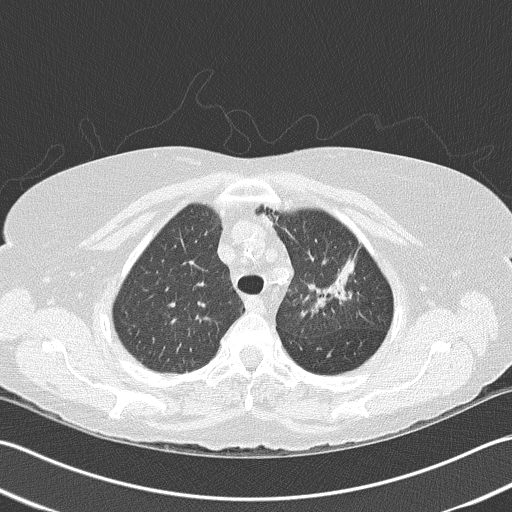
Chest CT (low-dose screening protocol), one axial image. Baseline screening round. Lung window (W 1500 / L -600 HU). 2 mm slice thickness. 512 × 512 image matrix. Female, age 68 years at enrolment. Former smoker at enrolment.
• Expert reader's lesion annotation, bounding box [x1, y1, x2, y2] px = [294, 239, 368, 318].
• Screening reader's record for this exam: no non-calcified nodule ≥4 mm recorded.
• Official screen result: negative screen, minor abnormalities not suspicious for lung cancer.